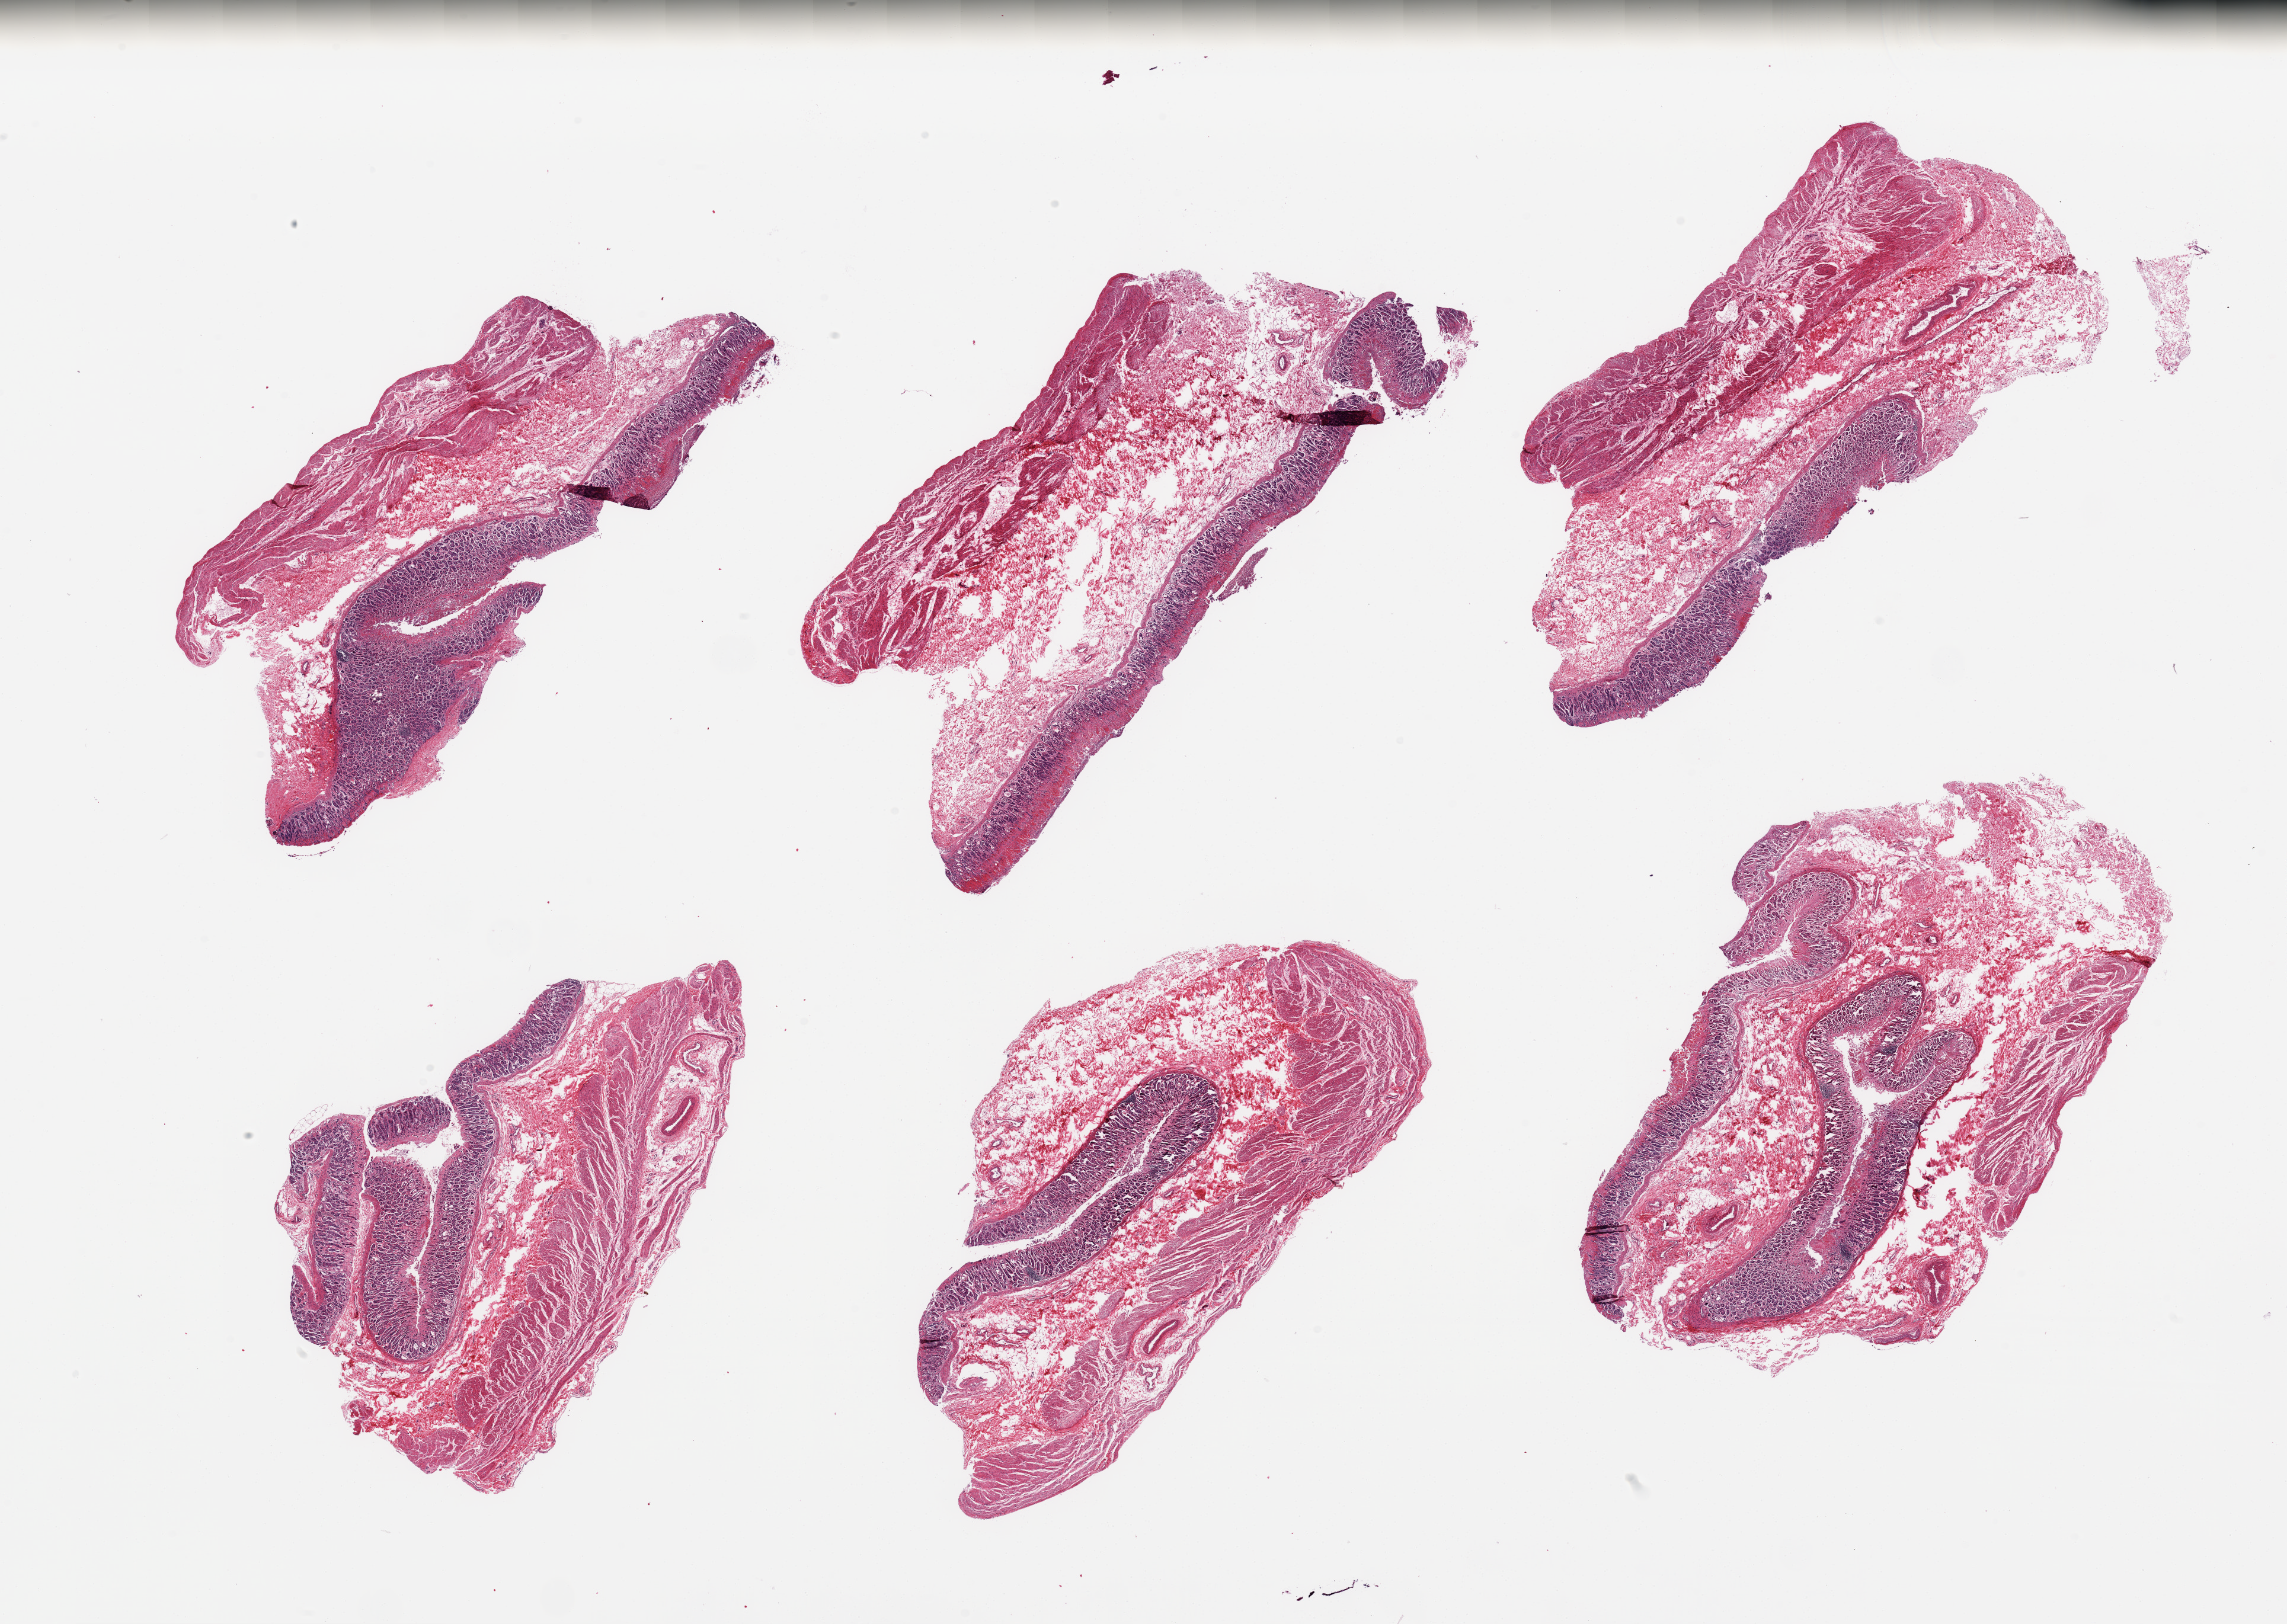
Whole-slide image, H&E stain — a low-resolution overview of the entire scanned area, about 30.5 x 21.7 mm, PAXgene-fixed paraffin-embedded (PFPE) section, target tissue: stomach, tissue donor sample. Donor: male.
Pathologist's review note for this sample: 6 pieces; microcystic glandular changes in mucosa with superficial autolysis/digestion.